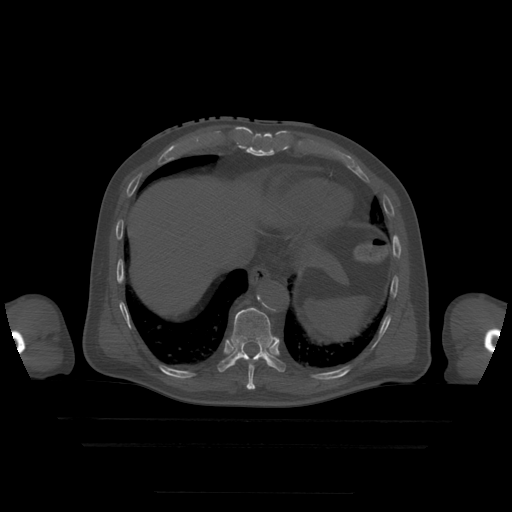
CT including the spine, one axial slice. Position 247 of 522 along the scan axis. Bone window (W 1800 / L 400 HU). 1.25 mm slice thickness. 512 × 512 image matrix, field of view 436 × 436 mm. Patient age 68 years. Case-level facts recorded for this patient, not image findings: primary cancer: urothelial.
Outlined on this slice (semi-automatic segmentation, software-assisted and operator-edited):
- T10 vertebra: bounding box (x1, y1, x2, y2) in pixels: (218, 308, 286, 373)
- T9 vertebra: (247, 361, 257, 390)